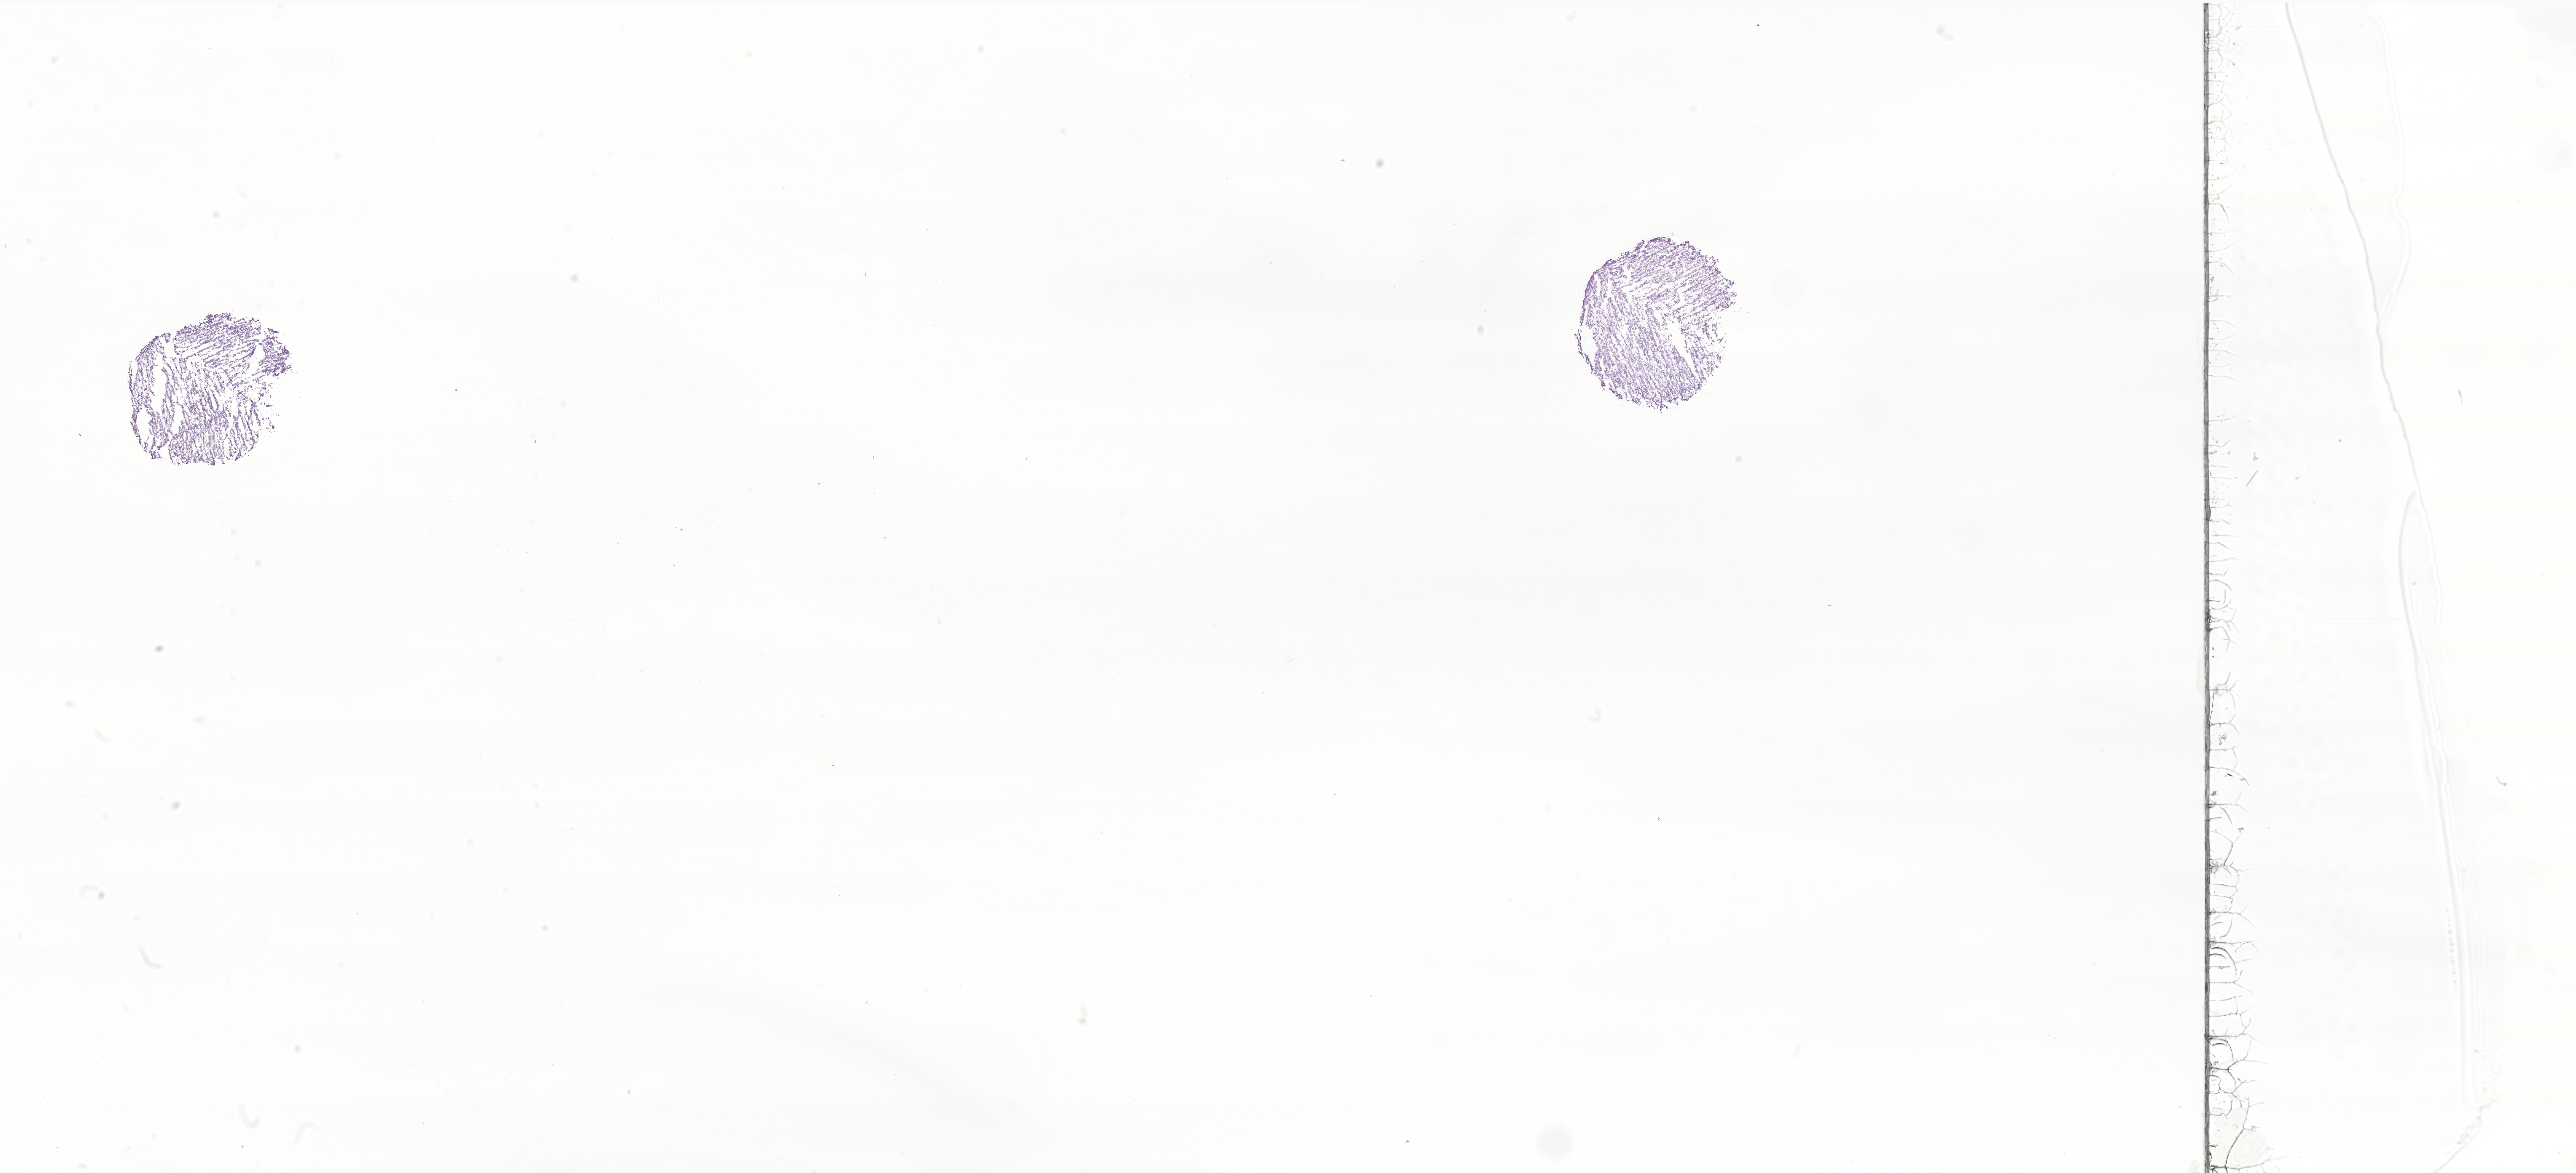
Haematoxylin and eosin whole-slide image of tumor tissue from the brain — low-resolution overview of the scanned area, about 36.6 x 16.7 mm, frozen section. Patient female; age 36 months.
Diagnosis (ICD-O-3 morphology term): Neoplasm, uncertain whether benign or malignant.